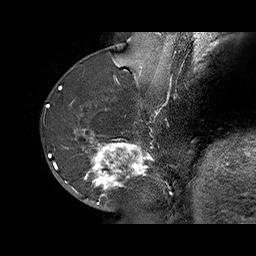
Breast MRI (dynamic contrast-enhanced), one sagittal slice. Slice 24 of 70 in the series (ordered by position). Dynamic contrast-enhanced series, time point 2 of 6 at this slice position (early post-contrast). 1.5 T. TE 4.5 ms, TR 32.4 ms. 3 mm slice thickness. 256 × 256 image matrix. Female patient. Case-level facts recorded for this patient, not image findings: setting: breast cancer imaged before/during neoadjuvant chemotherapy; receptor status: HR-positive, HER2-negative.
Structures marked on this image (semi-automatically segmented with operator editing):
- analysis volume of interest (the breast-tissue region the enhancement analysis was run in; not a lesion): box from (x=71, y=128) to (x=159, y=202) px
- tumour enhancement mask (voxels above the 100 % enhancement threshold inside the analysis volume of interest): (x=73, y=129)–(x=149, y=200)